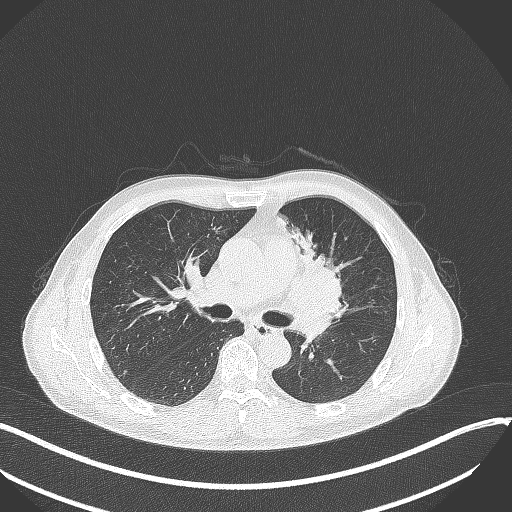
Chest CT, one axial slice; slice 200 of 411 in the series (ordered by position); reconstruction kernel B70f; 120 kVp; lung window (W 1500 / L -600 HU); 1 mm slice thickness; 512 × 512 image matrix, field of view 400 × 400 mm. Patient: male, 56 years. From the clinical record (not read from this slice): clinical TNM (as recorded): T2a N0 M0.
Outlined on this slice (bounding box drawn by a radiologist):
- lung tumour (recorded histology: squamous cell carcinoma): bounding box (x1, y1, x2, y2) in pixels: (288, 236, 351, 313)